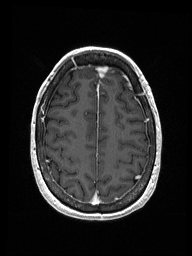
Brain MRI from a brain-tumour surgery series, one axial slice; position 45 of 192 along the scan axis; T1-weighted post-contrast; 192 × 256 image matrix, field of view 187 × 250 mm. Case-level facts recorded for this patient, not image findings: histopathology: Metastastic Carcinoma from Breast primary; tumour location: Right Frontal.
Outlined on this slice (expert manual segmentation):
- previous resection cavity: bounding box (x1, y1, x2, y2) in pixels: (98, 66, 108, 70)